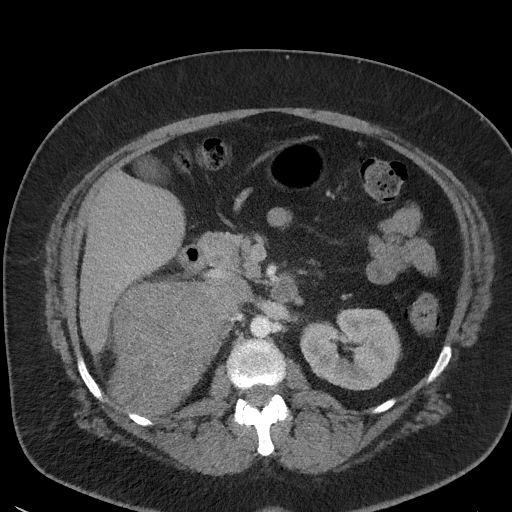
Contrast-enhanced abdominal CT, one axial slice. Position 25 of 56 along the scan axis. 120 kVp. Intravenous contrast given. Soft-tissue window (W 400 / L 40 HU). 512 × 512 image matrix. Patient: female, 35 years. Case-level facts recorded for this patient, not image findings: diagnosis: adrenocortical carcinoma; tumour side: right adrenal; tumour size at pathology: 15 cm; Ki-67 index: 40 %; stage (as recorded): 2.
Outlined on this slice (semi-automatically segmented with operator editing):
- mass: box from (x=115, y=280) to (x=239, y=414) px